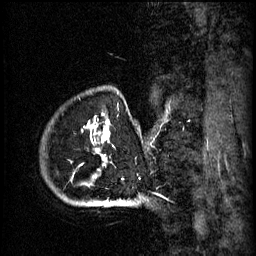
Breast MRI (dynamic contrast-enhanced), one sagittal slice. Position 55 of 60 along the scan axis. 3 images stored at this slice position (order not interpretable as contrast timing). 1.5 T. TE 4.2 ms, TR 11 ms. 2 mm slice thickness. 256 × 256 image matrix, field of view 200 × 200 mm. Female patient, age 51 years.
Annotated regions visible in this slice (semi-automatically segmented with operator editing):
- analysis volume of interest (the breast-tissue region the enhancement analysis was run in; not a lesion): bounding box [x1, y1, x2, y2] px = [51, 90, 161, 197]
- tumour enhancement mask (voxels above the 70 % enhancement threshold inside the analysis volume of interest): [98, 114, 110, 159]